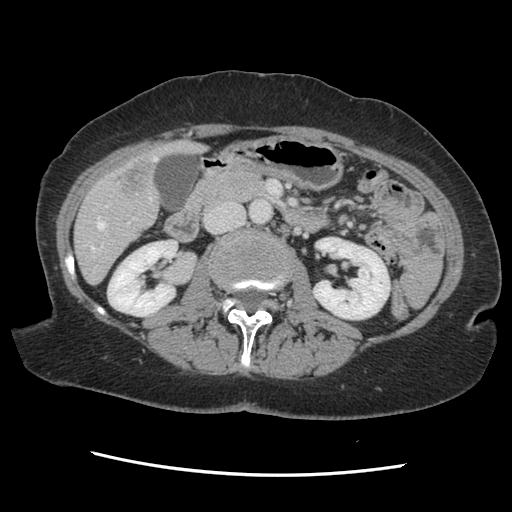
Contrast-enhanced abdominal CT, one axial slice. 120 kVp. Soft-tissue window (W 400 / L 40 HU). 2.5 mm slice thickness. 512 × 512 image matrix, field of view 330 × 330 mm. Female patient, age 61 years. From the clinical record (not read from this slice): diagnosis: colorectal cancer liver metastases, imaged before liver resection; multiple liver metastases: no; largest metastasis: 2.4 cm; disease in both lobes: no.
Outlined on this slice (outlined manually by an expert reader):
- hepatic veins: box from (x=90, y=157) to (x=157, y=258) px
- liver: (x=75, y=141)–(x=202, y=282)
- planned liver remnant (the part of the liver to remain after resection): (x=75, y=193)–(x=159, y=282)
- portal vein (with intrahepatic branches): (x=102, y=222)–(x=130, y=247)
- liver metastasis: (x=116, y=160)–(x=151, y=197)